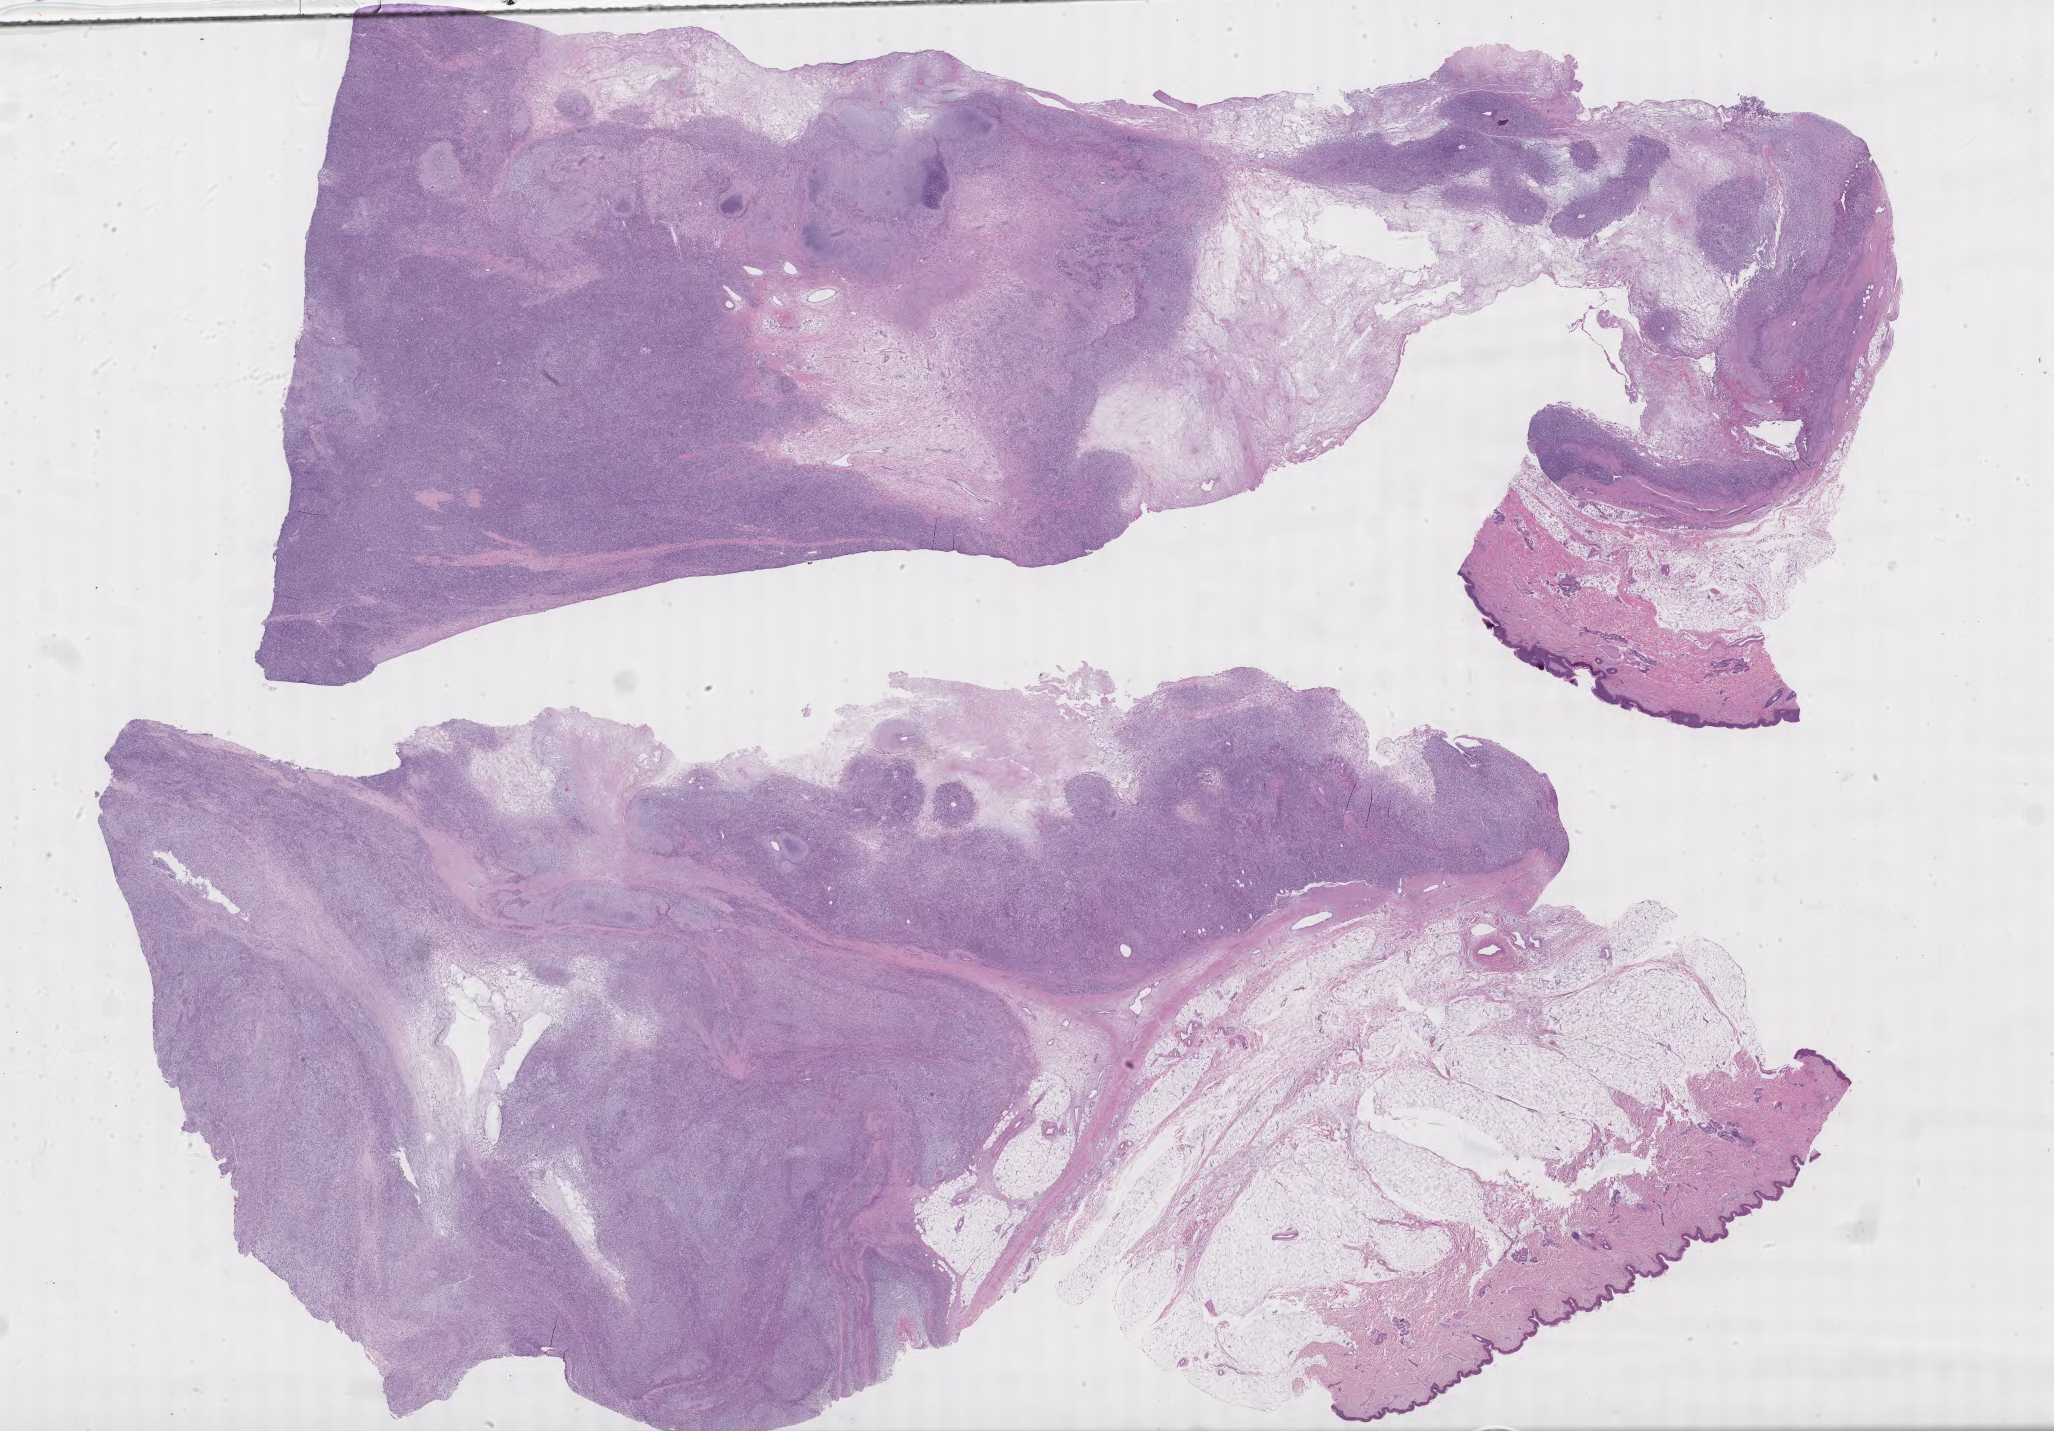
Hematoxylin and eosin (H&E) whole-slide image of tumor tissue from the soft tissue of upper extremity — low-resolution overview of the scanned area, about 33.2 x 23.1 mm; FFPE section. Male patient, age 300 days.
Diagnosis: Sarcoma, NOS.